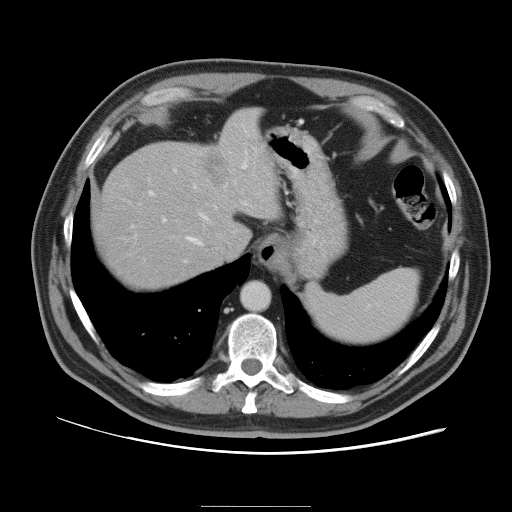
Contrast-enhanced abdominal CT, one axial slice; position 80 of 105 along the scan axis; 120 kVp; intravenous contrast given; soft-tissue window (W 400 / L 40 HU); 5 mm slice thickness; 512 × 512 image matrix, field of view 399 × 399 mm. Male patient, age 64 years. From the clinical record (not read from this slice): diagnosis: colorectal cancer liver metastases, imaged before liver resection; multiple liver metastases: yes; largest metastasis: 3 cm; disease in both lobes: yes.
Structures marked on this image (expert manual segmentation):
- hepatic veins: bounding box [x1, y1, x2, y2] px = [186, 212, 210, 245]
- liver: [95, 110, 276, 289]
- planned liver remnant (the part of the liver to remain after resection): [94, 149, 229, 288]
- portal vein (with intrahepatic branches): [132, 163, 247, 262]
- liver metastasis: [205, 150, 229, 187]